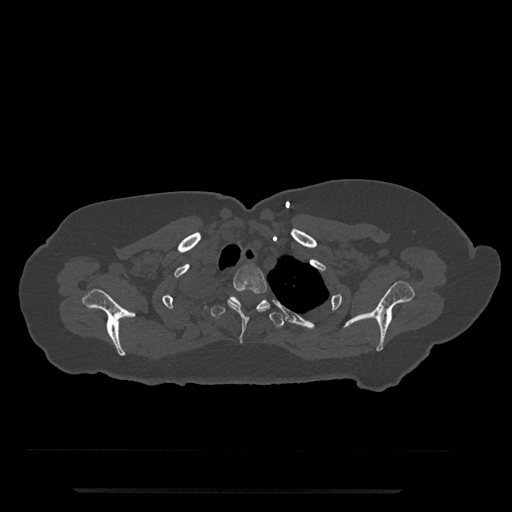
CT including the spine, one axial slice. Position 659 of 797 along the scan axis. Reconstruction kernel Br40s/3. 120 kVp. Bone window (W 1800 / L 400 HU). 512 × 512 image matrix. Patient: female, 51 years. From the clinical record (not read from this slice): primary cancer: neuro; vertebrae with lytic lesions (as recorded): T8.
Structures marked on this image (semi-automatically segmented with operator editing):
- T2 vertebra: bounding box <227,264,267,343> (left, top, right, bottom; pixels)
- T3 vertebra: <211,295,284,328>